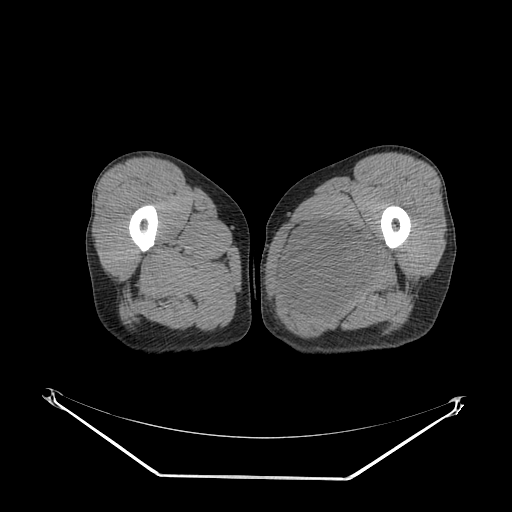
CT of an extremity soft-tissue mass (from a PET/CT study), one axial slice; slice 27 of 267 in the series (ordered by position); 140 kVp; soft-tissue window (W 400 / L 40 HU); 3.75 mm slice thickness; 512 × 512 image matrix, field of view 500 × 500 mm. Male patient. Case-level facts recorded for this patient, not image findings: histological type: pleiomorphic liposarcoma; grade: high; site of the primary tumour: left thigh.
Outlined on this slice (expert contour drawn on MRI and transferred to this co-registered scan by the dataset authors):
- gross tumour volume including surrounding oedema: bounding box (x1, y1, x2, y2) in pixels: (285, 217, 384, 316)
- gross tumour volume (mass): (288, 222, 376, 309)